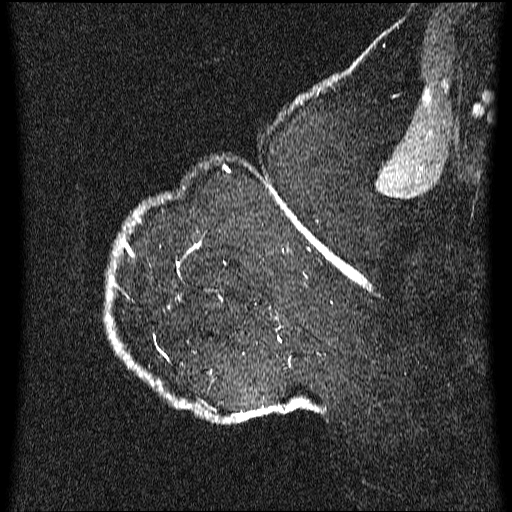
Breast MRI (dynamic contrast-enhanced), one sagittal slice. Position 51 of 64 along the scan axis. Dynamic contrast-enhanced series, image 2 of 3 at this slice position (ordered by acquisition). 1.5 T. TE 4.2 ms, TR 9.1 ms. 512 × 512 image matrix, field of view 180 × 180 mm. Patient: female, 52 years.
Outlined on this slice (semi-automatic segmentation, software-assisted and operator-edited):
- analysis volume of interest (the breast-tissue region the enhancement analysis was run in; not a lesion): bounding box (x1, y1, x2, y2) in pixels: (104, 203, 350, 425)
- tumour enhancement mask (voxels above the 70 % enhancement threshold inside the analysis volume of interest): (108, 203, 350, 423)